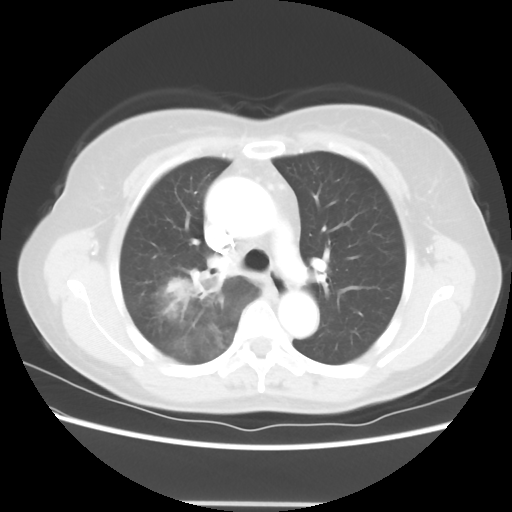
Chest CT, one axial slice. Slice 40 of 56 in the series (ordered by position). Reconstruction kernel STANDARD. 120 kVp. Lung window (W 1500 / L -600 HU). 512 × 512 image matrix, field of view 360 × 360 mm. Female patient, age 55 years. From the clinical record (not read from this slice): clinical TNM (as recorded): T2 N1 M0; histopathological grade: G2-3.
Outlined on this slice (rectangle marked by the reading radiologist):
- lung tumour (recorded histology: adenocarcinoma): bounding box (x1, y1, x2, y2) in pixels: (157, 266, 225, 329)